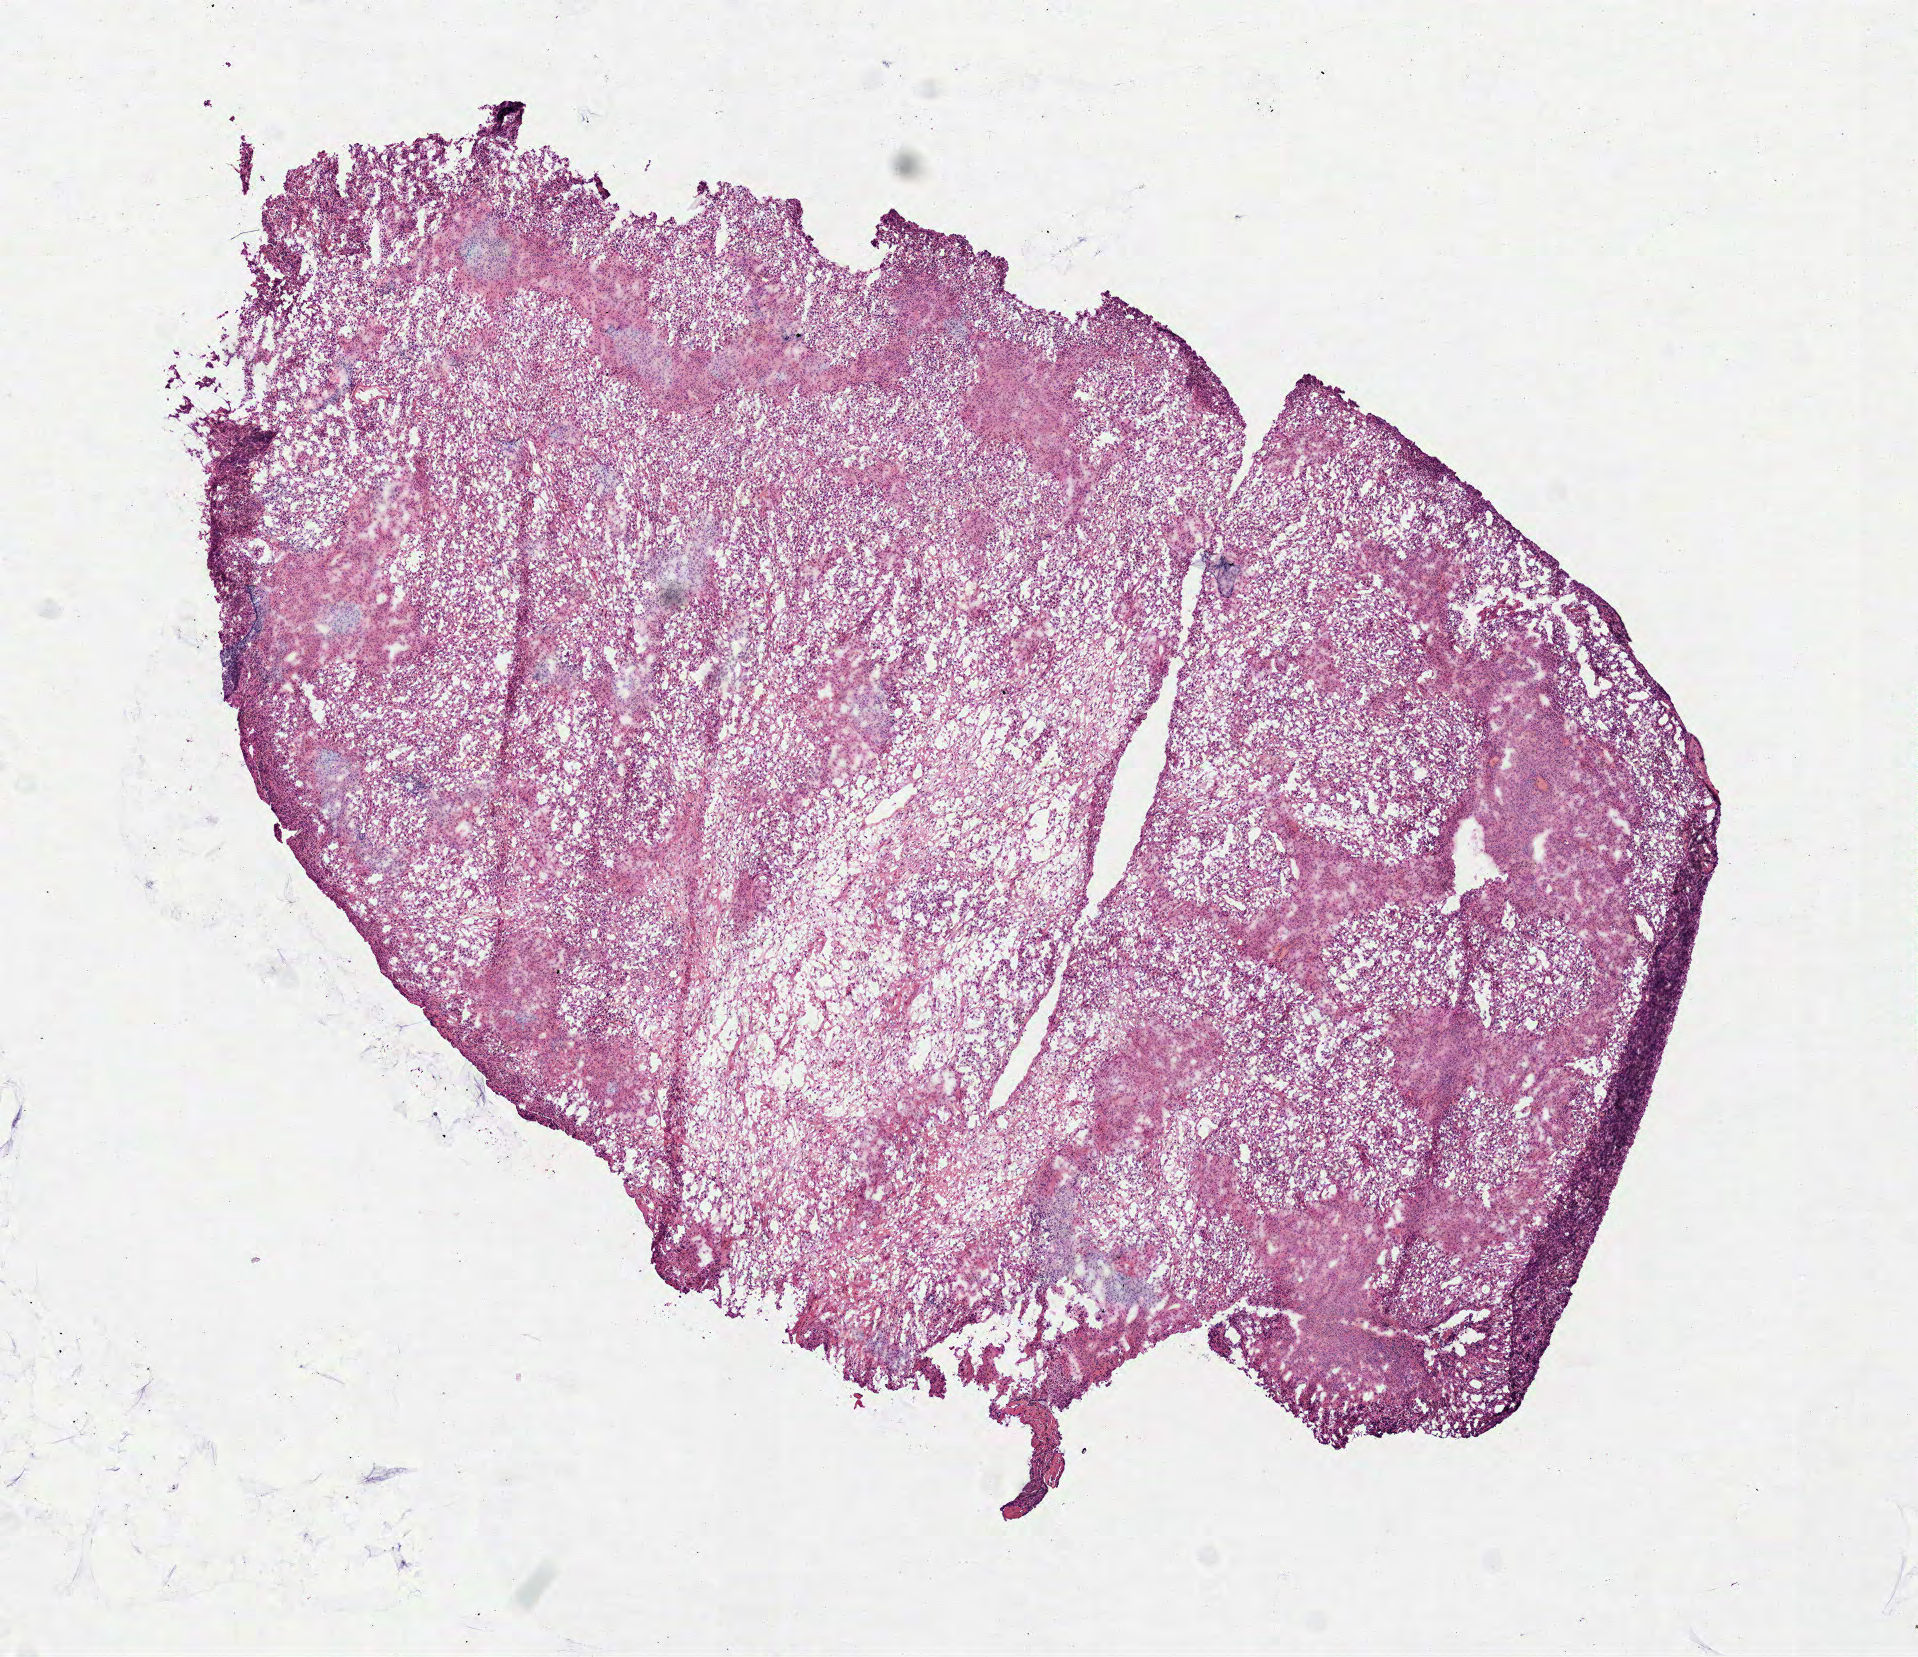
Digitized Hematoxylin and eosin (H&E) stained tissue section (whole slide), whole scanned area (about 7.7 x 6.7 mm, acquisition: 40x scan) shown as a low-resolution overview, frozen section from the top of the tissue portion, primary tumour sample from the lymphoid tissue. Male patient; age at initial diagnosis 69 years. Pathologist review of this section (percent, as recorded): tumour cells 85%, tumour nuclei 75%, normal cells 0%, stromal cells 15%, necrosis 0%.
- histologic diagnosis: Diffuse large B-cell lymphoma, NOS (intra-abdominal lymph nodes)